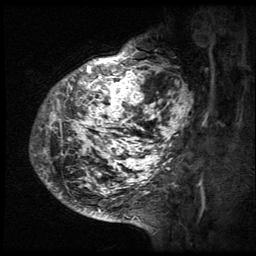
Breast MRI (dynamic contrast-enhanced), one sagittal slice. Slice 16 of 64 in the series (ordered by position). 3 images stored at this slice position (order not interpretable as contrast timing). 1.5 T. TE 4.2 ms, TR 9 ms. 2.5 mm slice thickness. 256 × 256 image matrix. Patient: female, 50 years. Case-level facts recorded for this patient, not image findings: setting: breast cancer imaged before/during neoadjuvant chemotherapy; receptor status: triple-negative.
Outlined on this slice (semi-automatic segmentation, software-assisted and operator-edited):
- analysis volume of interest (the breast-tissue region the enhancement analysis was run in; not a lesion): bounding box <30,39,194,212> (left, top, right, bottom; pixels)
- tumour enhancement mask (voxels above the 140 % enhancement threshold inside the analysis volume of interest): <31,41,194,212>